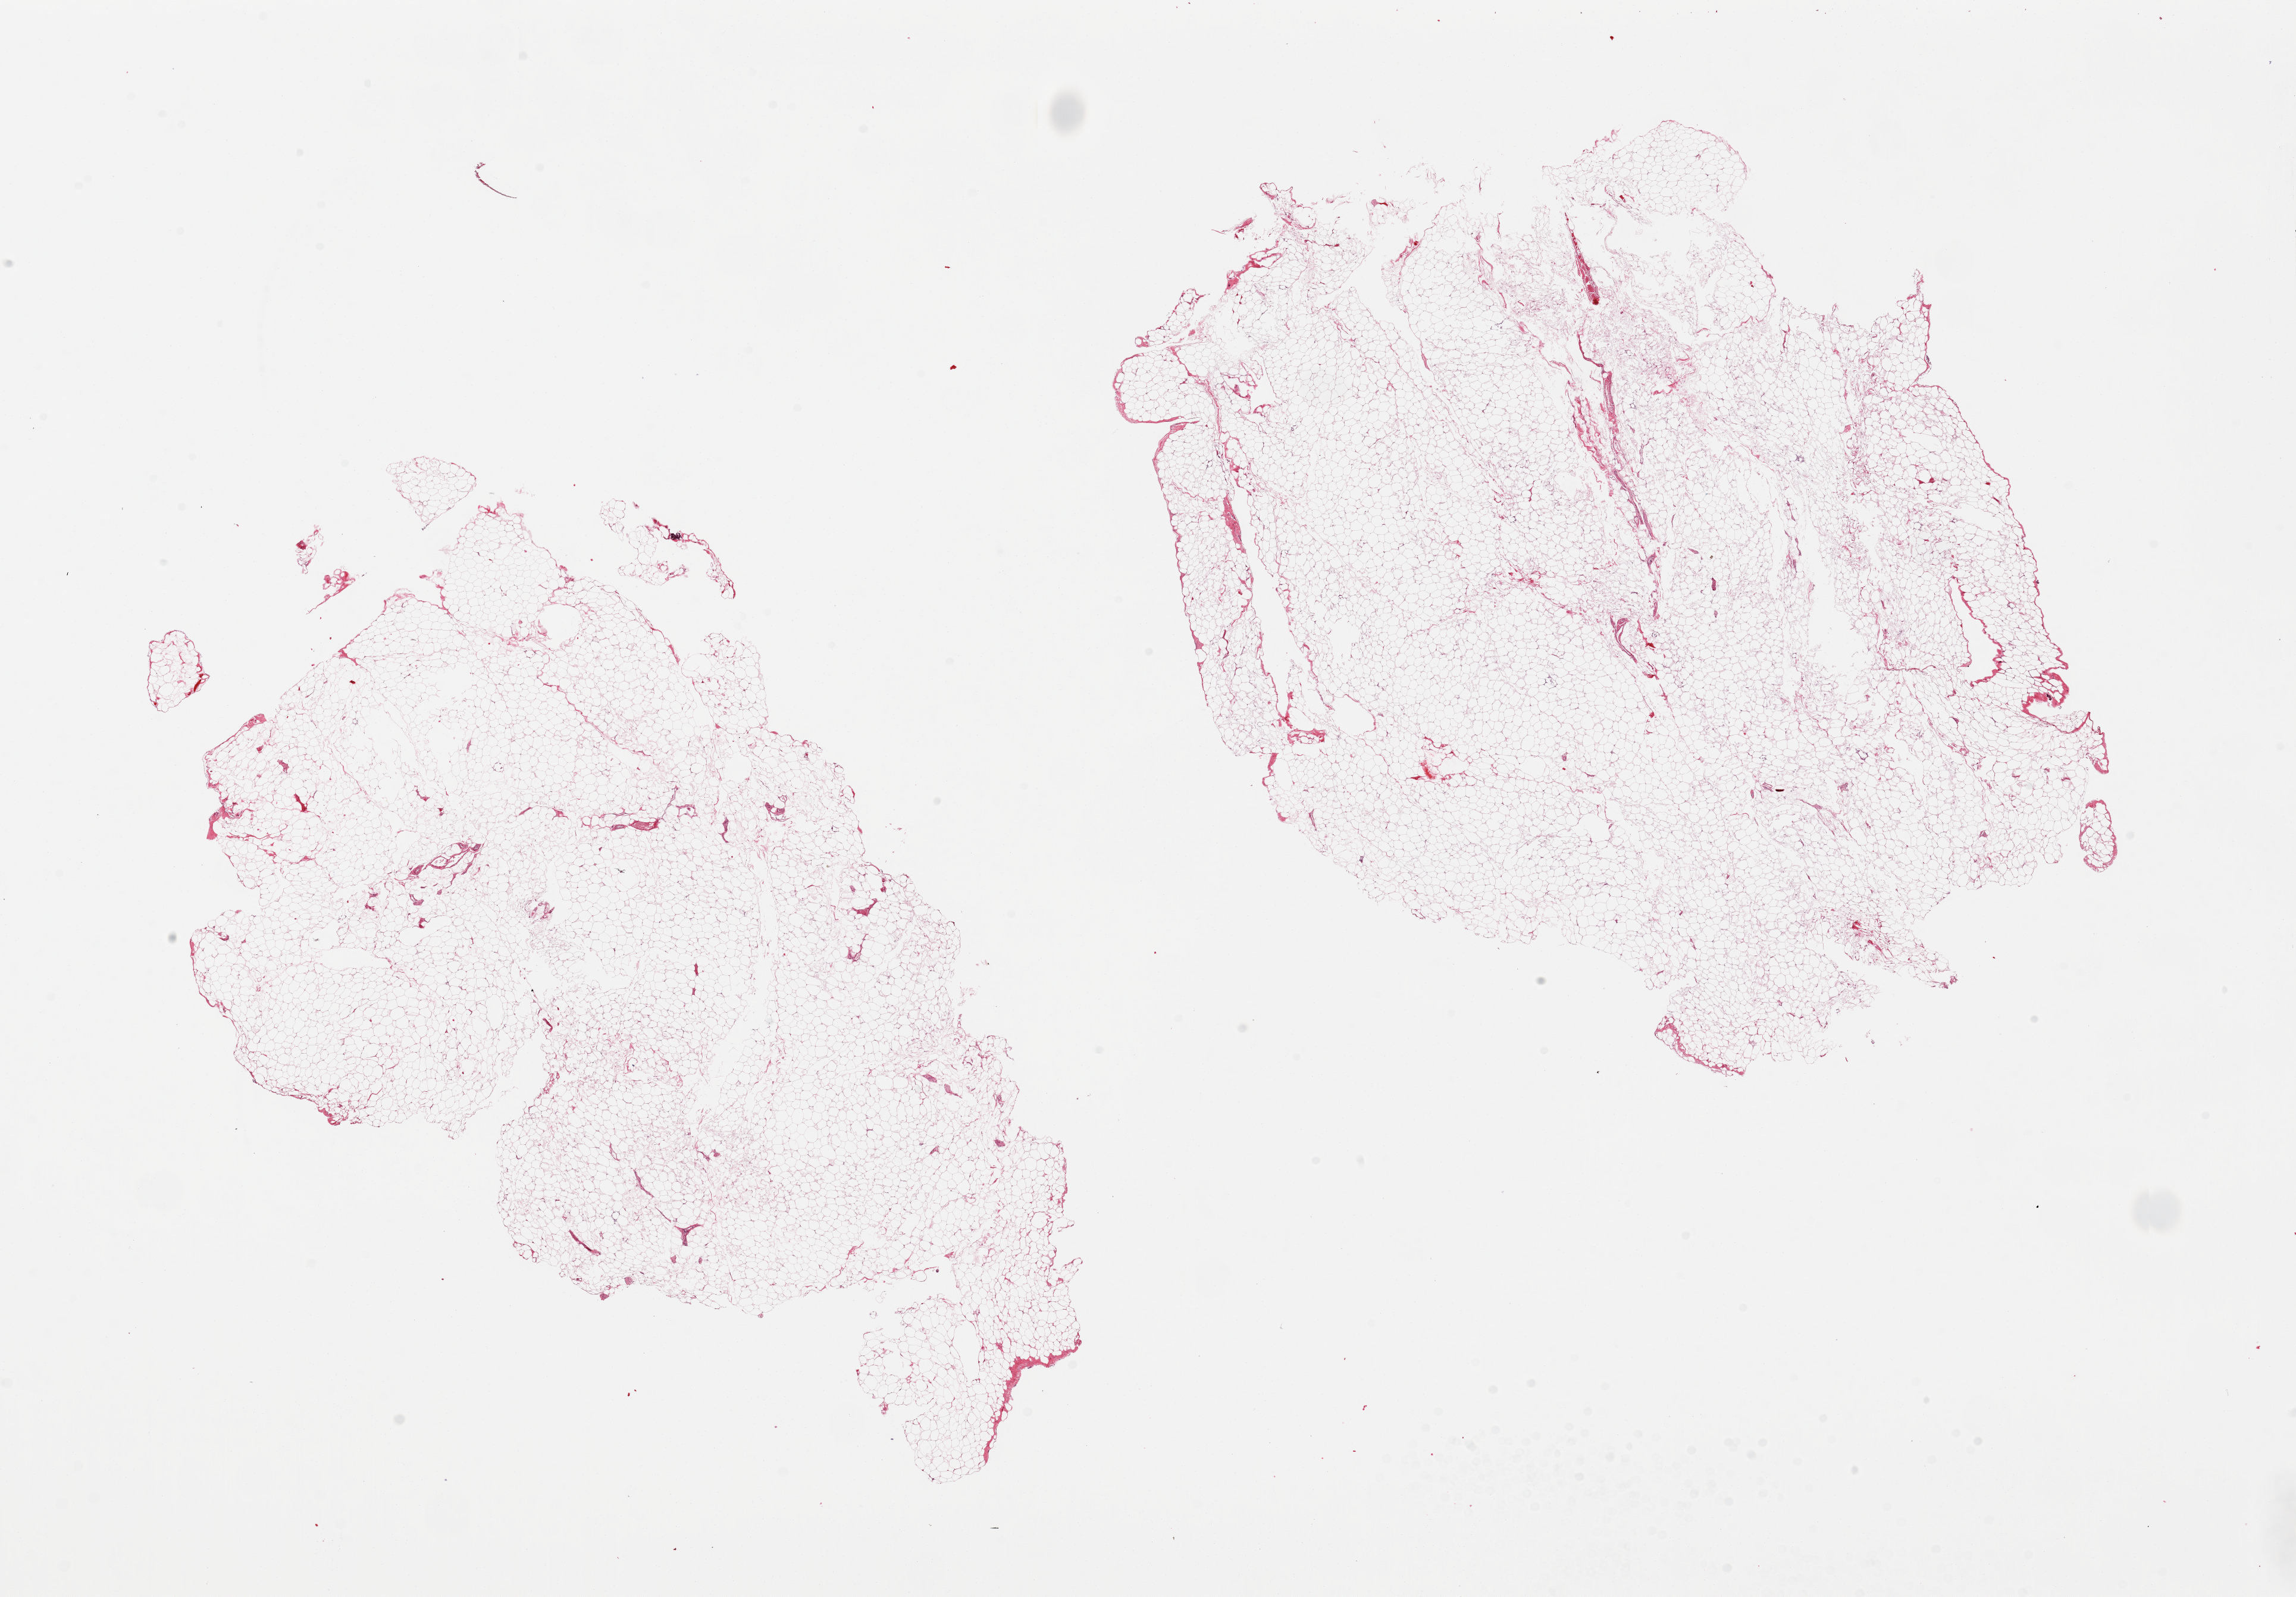
Digitized hematoxylin and eosin (H&E)-stained section, a low-resolution overview of the entire scanned area, about 30.5 x 21.2 mm (slide scanned at 20x), PAXgene-fixed, paraffin-embedded tissue, section of omentum (target tissue), tissue donor sample. Male donor.
Pathologist's review note for this sample: 2 pieces.